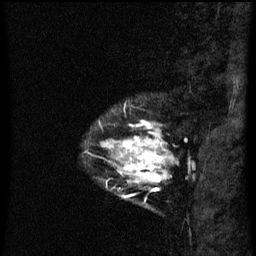
Breast MRI (dynamic contrast-enhanced), one sagittal slice; position 11 of 60 along the scan axis; dynamic contrast-enhanced series, image 2 of 3 at this slice position (ordered by acquisition); 1.5 T; TE 4.2 ms, TR 8 ms; 256 × 256 image matrix. Female patient, age 33 years.
Outlined on this slice (semi-automatically segmented with operator editing):
- analysis volume of interest (the breast-tissue region the enhancement analysis was run in; not a lesion): bounding box (x1, y1, x2, y2) in pixels: (107, 120, 163, 199)
- tumour enhancement mask (voxels above the 70 % enhancement threshold inside the analysis volume of interest): (107, 120, 163, 199)